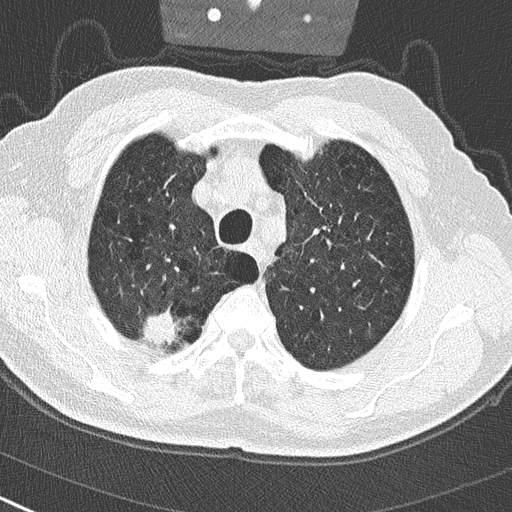
Chest CT (low-dose screening protocol), one axial image, first (baseline) screen, lung window (W 1500 / L -600 HU), 2 mm slice thickness, lung (sharp) reconstruction kernel (B50f), slice 55 of 290 in the series, 512 × 512 image matrix, field of view 300 × 300 mm. Male participant, aged 65 years at enrolment. Current smoker at enrolment.
- Expert reader's lesion annotation, bounding box <135,303,187,353> (left, top, right, bottom; pixels).
- The exam's reader record, not a measurement of the box and not confirmed to be the same lesion: non-calcified nodule or mass ≥4 mm, right upper lobe, 24 × 19 mm, spiculated (stellate) margins, soft tissue attenuation.